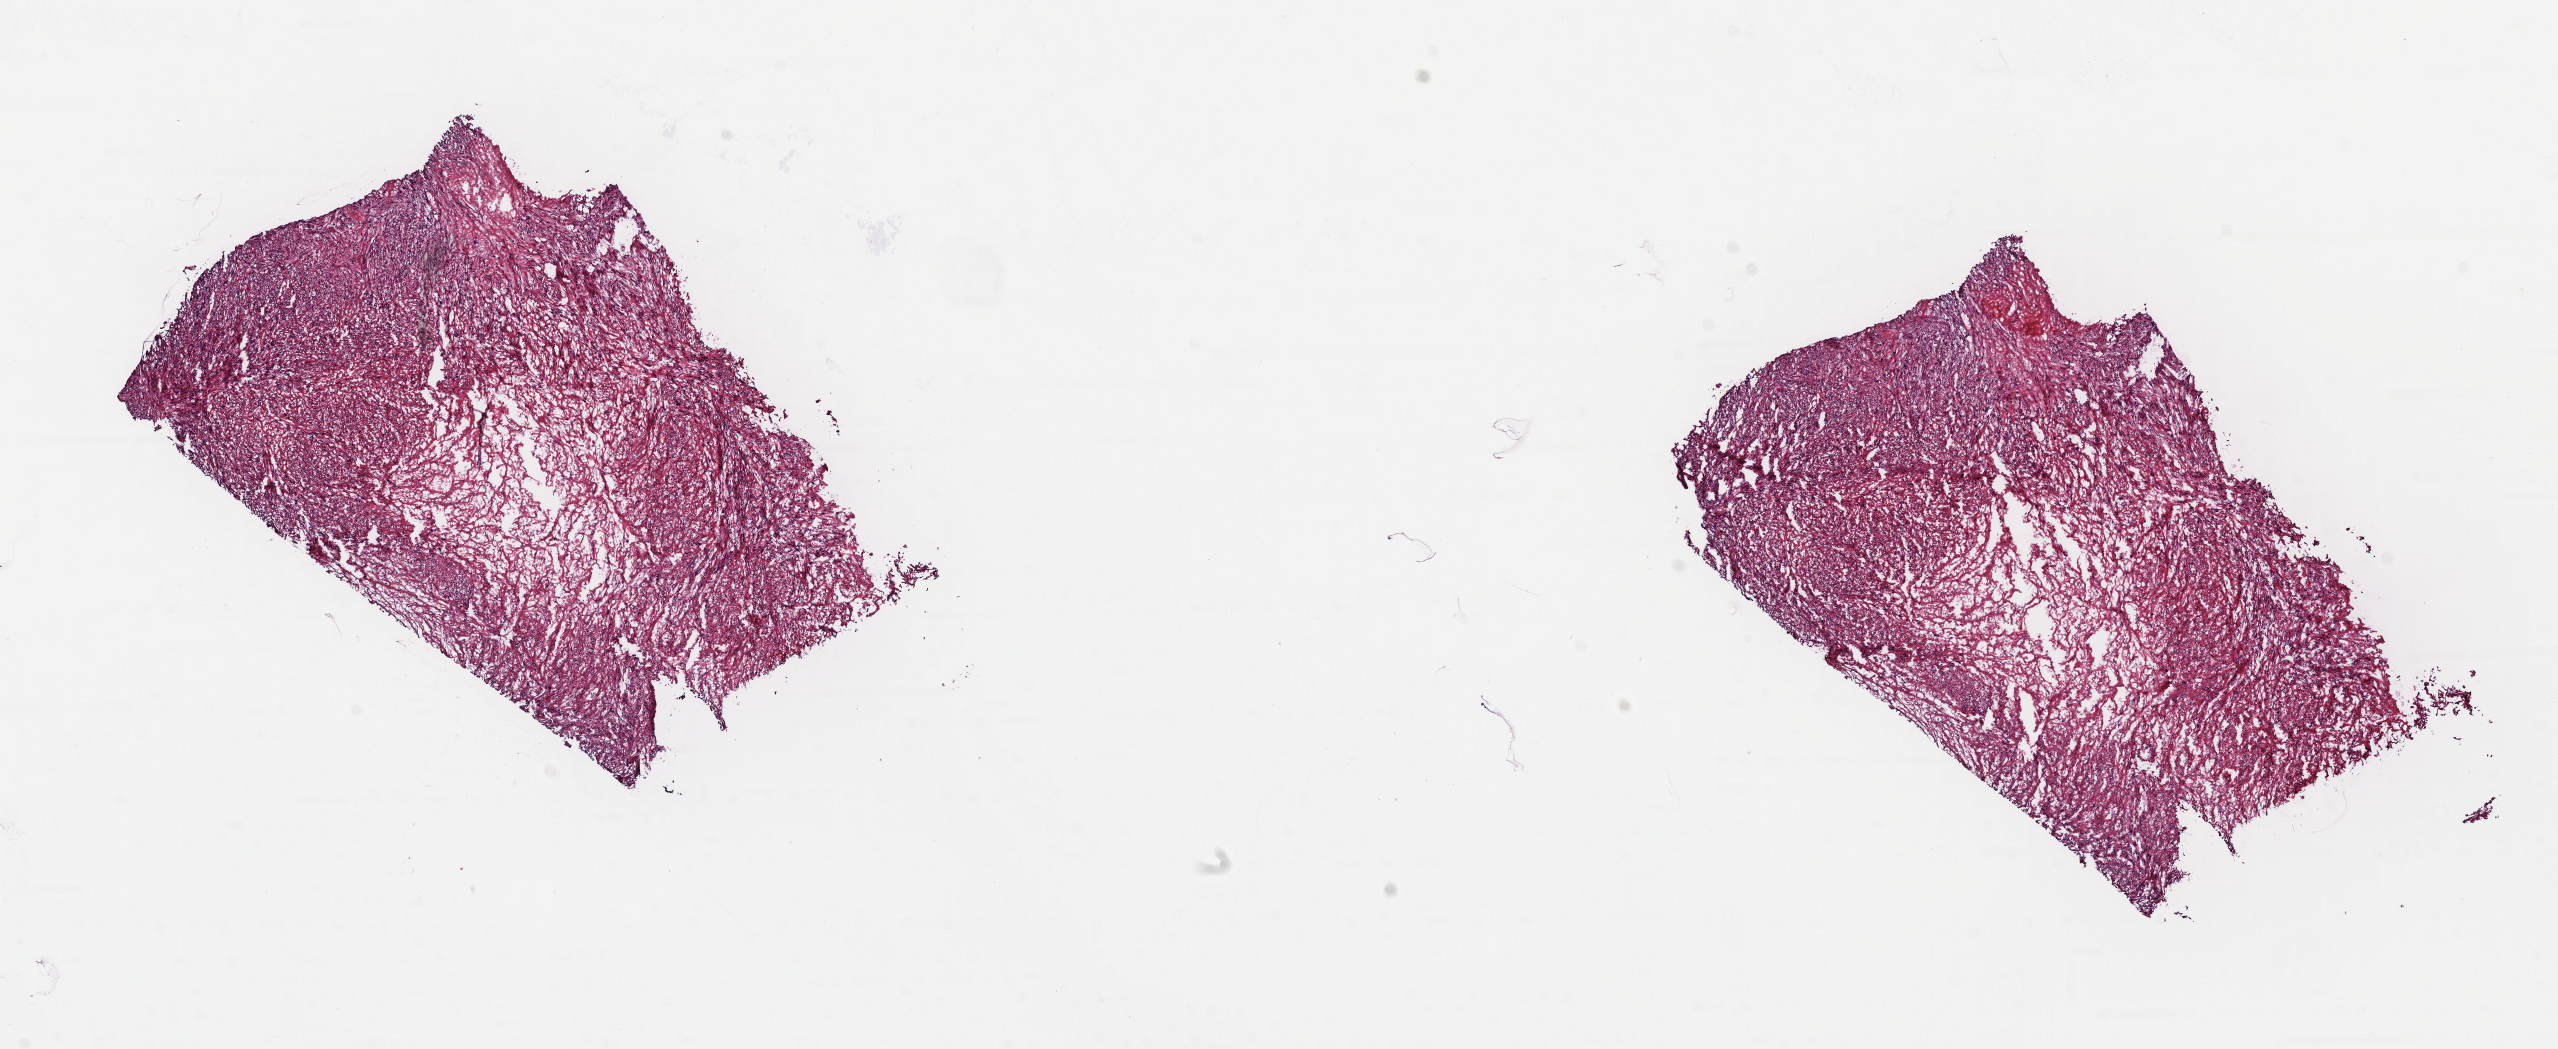
Whole-slide histology image, H&E-stained — low-resolution overview of the scanned area, about 20.1 x 8.2 mm (acquisition: 40x scan); frozen section from the top of the tissue portion; primary tumour sample from the retroperitoneum and peritoneum. Patient: female, age at initial diagnosis 59 years. Composition of this section per pathologist review: tumour cells 70%, tumour nuclei 100%, normal cells 0%, stromal cells 30%, necrosis 0%. Infiltration values recorded for this section: lymphocyte infiltration 0%, monocyte infiltration 0%, neutrophil infiltration 0%.
• pathologic diagnosis: Leiomyosarcoma, NOS (retroperitoneum)